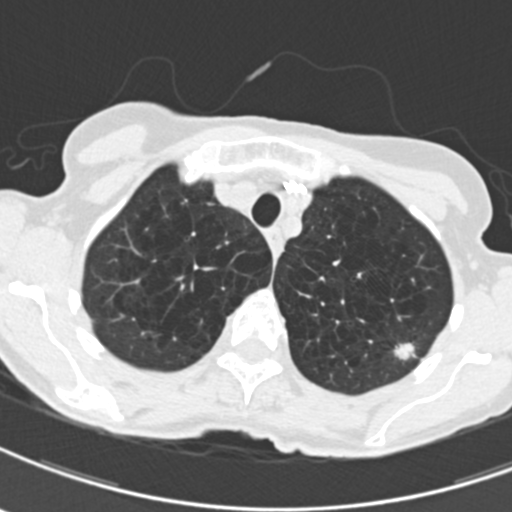
Low-dose screening chest CT, one axial slice; slice 165 of 203 in the series (ordered by position); reconstruction kernel B30f; lung window (W 1500 / L -600 HU); 2 mm slice thickness; 512 × 512 image matrix, field of view 279 × 279 mm.
Outlined on this slice (manually delineated by an expert):
- lesion 1 (tumor, upper lobe of left lung): bounding box [x1, y1, x2, y2] px = [393, 343, 416, 361]